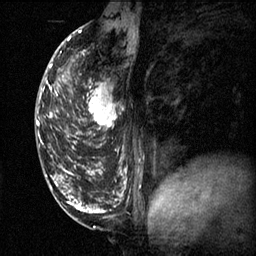
Breast MRI (dynamic contrast-enhanced), one sagittal slice. Position 31 of 60 along the scan axis. 3 images stored at this slice position (order not interpretable as contrast timing). 1.5 T. TE 4.2 ms, TR 11.1 ms. 2 mm slice thickness. 256 × 256 image matrix. Patient: female, 50 years.
Outlined on this slice (semi-automatically segmented with operator editing):
- analysis volume of interest (the breast-tissue region the enhancement analysis was run in; not a lesion): bounding box <68,68,127,141> (left, top, right, bottom; pixels)
- tumour enhancement mask (voxels above the 70 % enhancement threshold inside the analysis volume of interest): <68,74,121,139>